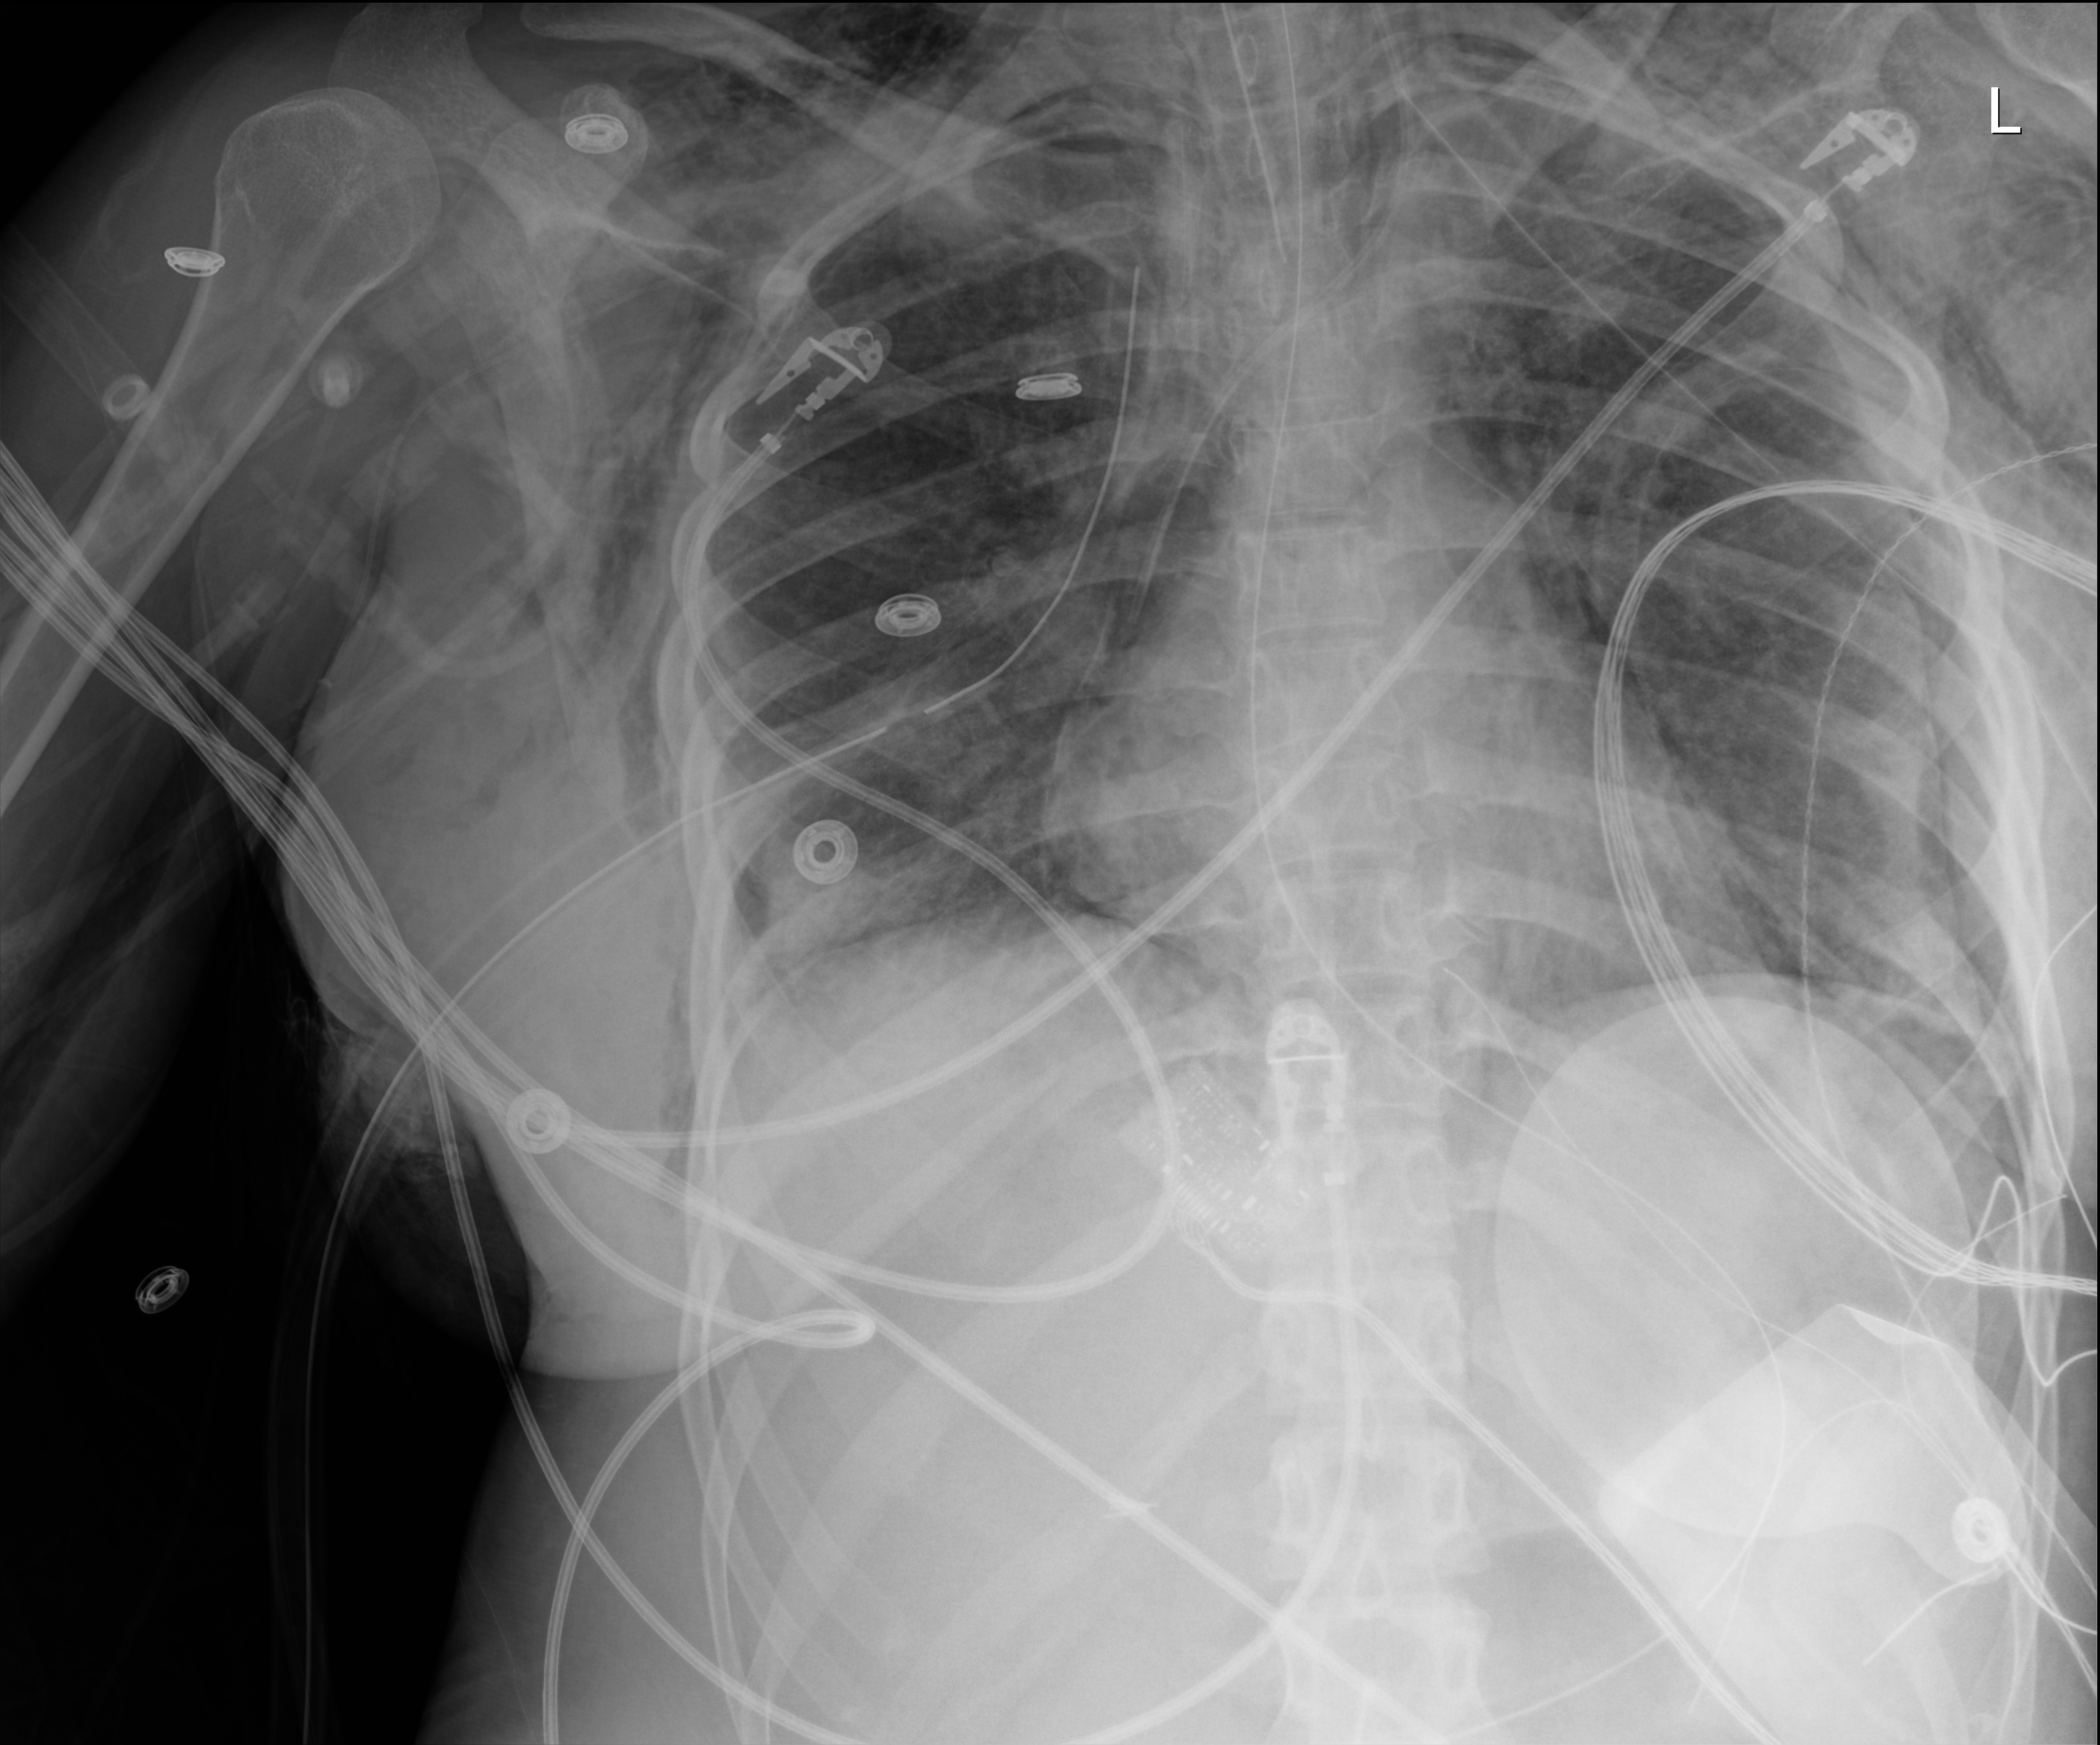
Bedside chest radiograph (digital radiography); anteroposterior (AP) projection. Patient hospitalised with COVID-19, aged 18–59 years.
Admission-level facts for this patient (not findings on this image; timing relative to this image not recorded):
- admitted to intensive care during this hospital stay: yes
- mechanically ventilated during this hospital stay: yes